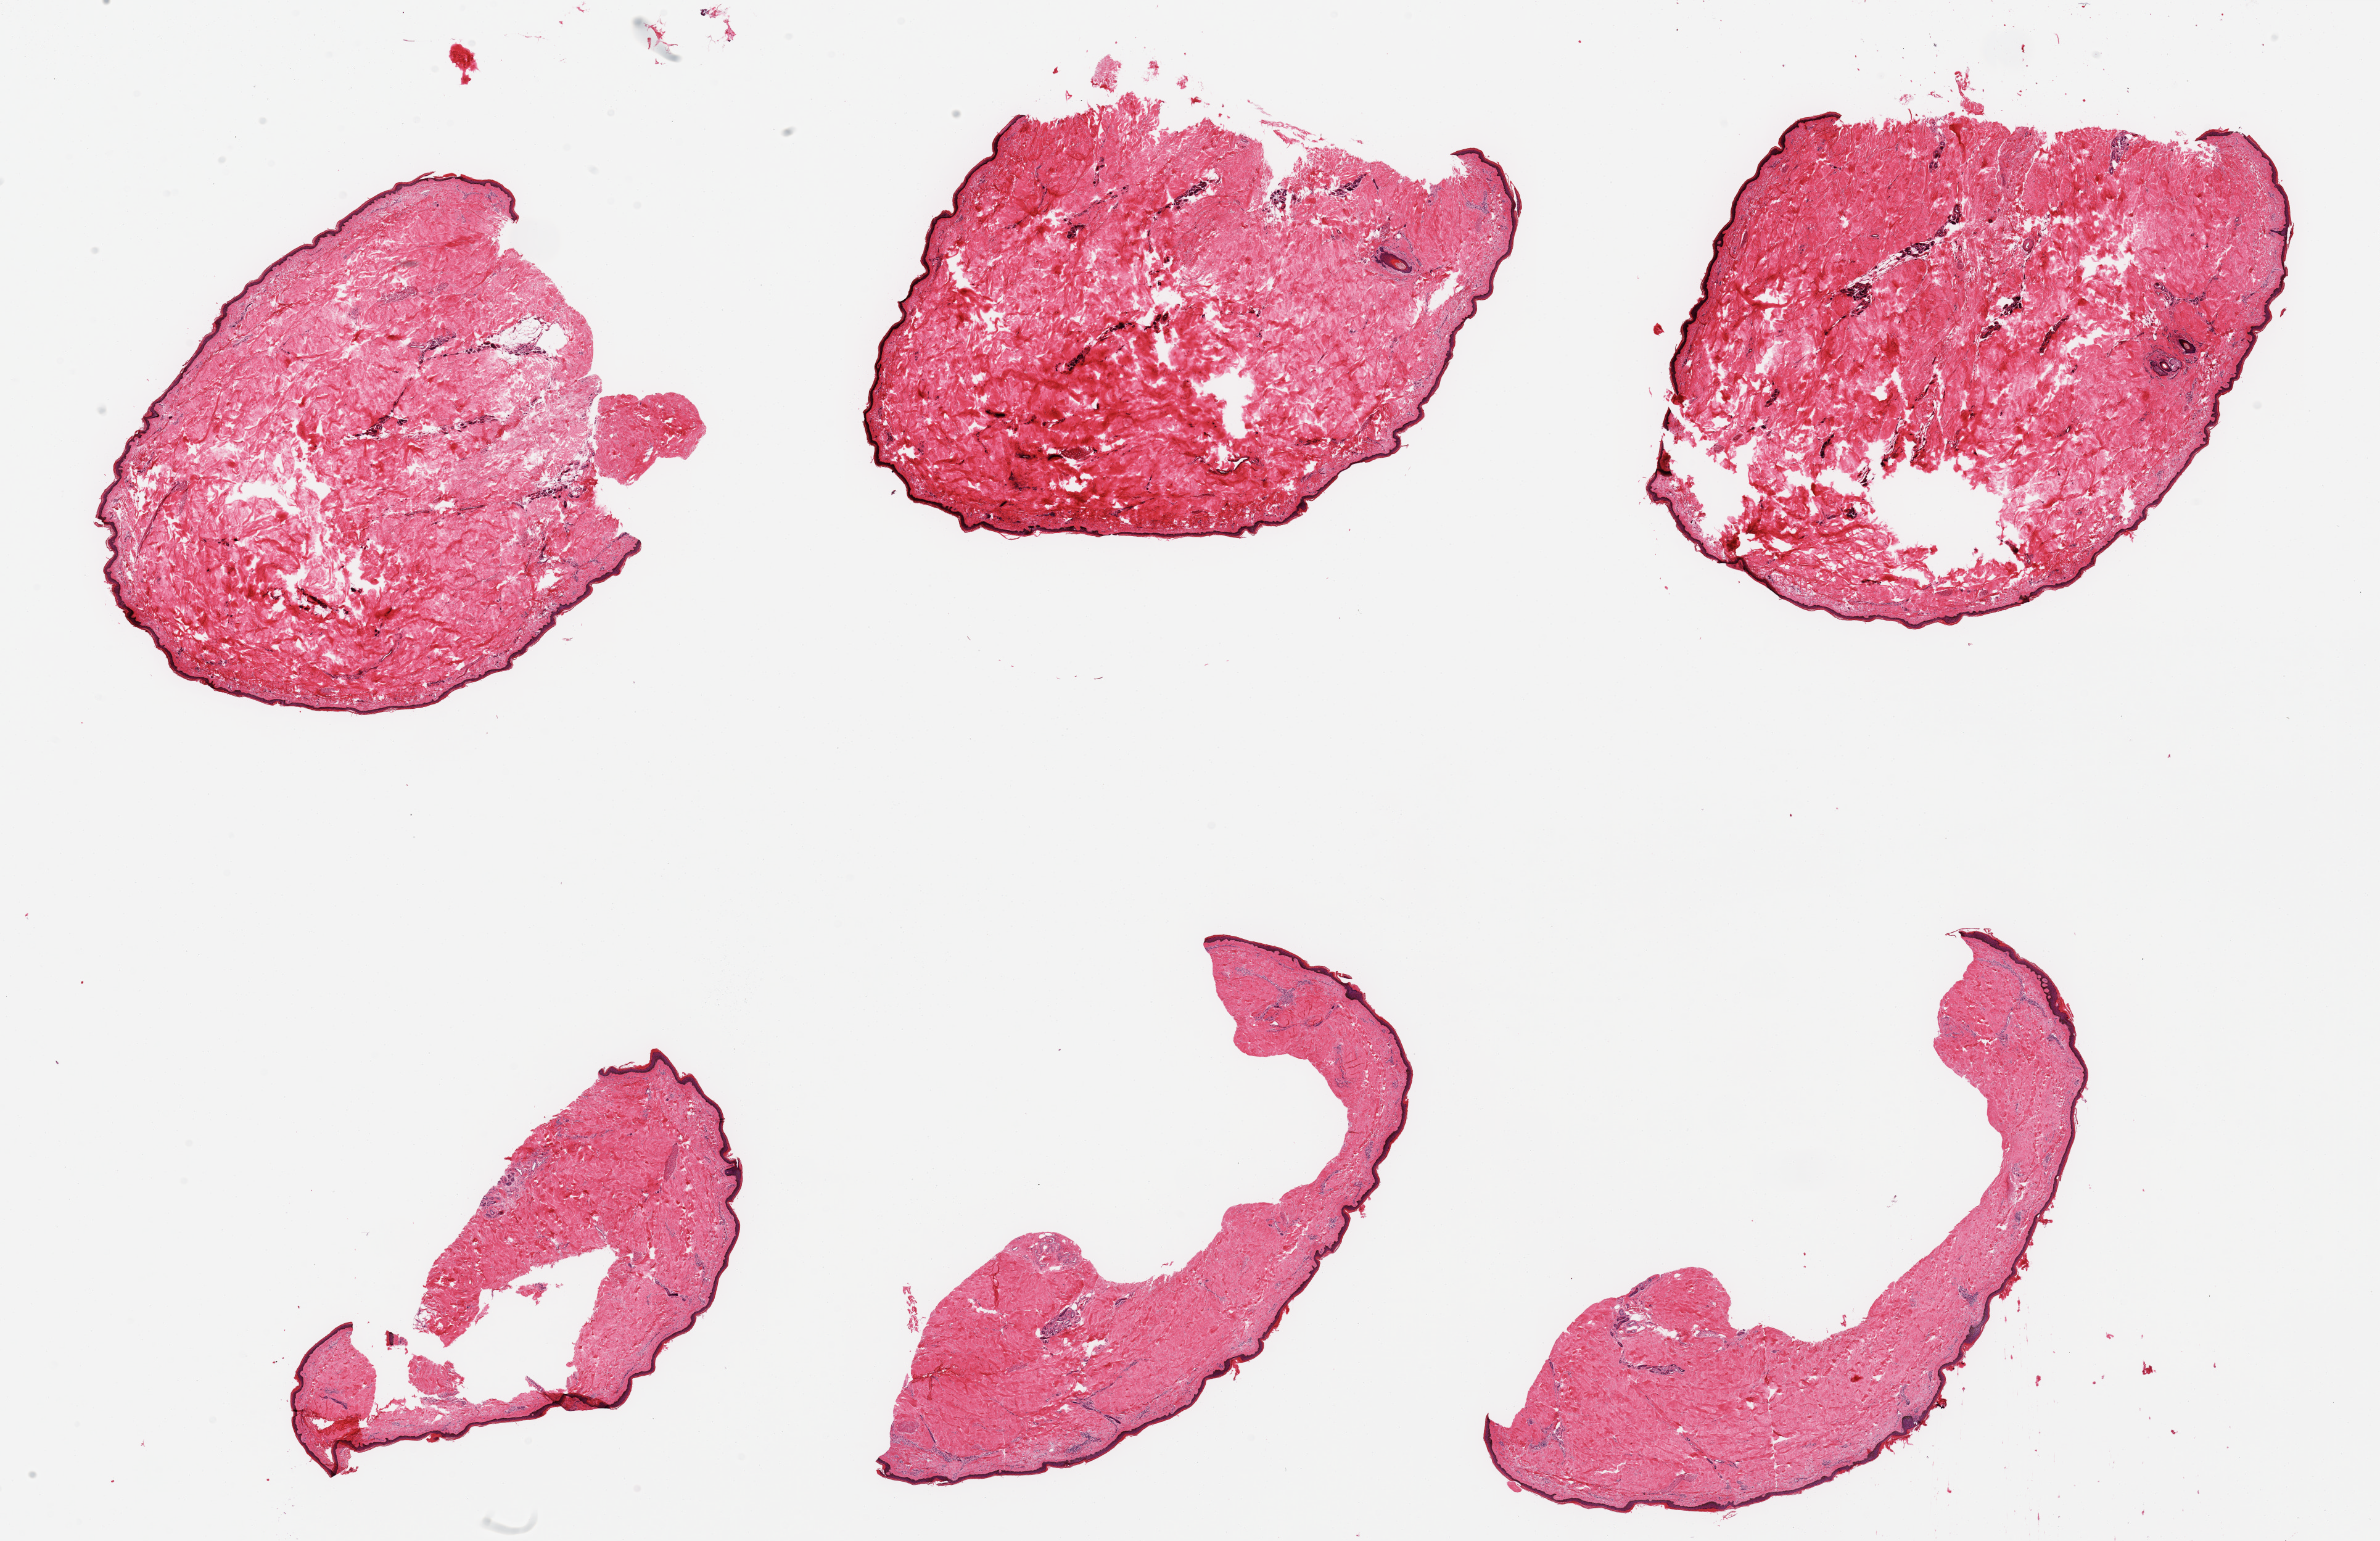
Whole-slide image, H&E stain — shown as a low-resolution overview of the whole scanned area (about 30.5 x 19.8 mm, from a 20x scan), PAXgene-fixed paraffin-embedded (PFPE) section, sampled site (target tissue): skin of lower leg, tissue donor sample. Male donor.
- reviewer comment on this tissue sample: 6 pieces, no dermal fat; squamous epithelium is ~40-50 microns